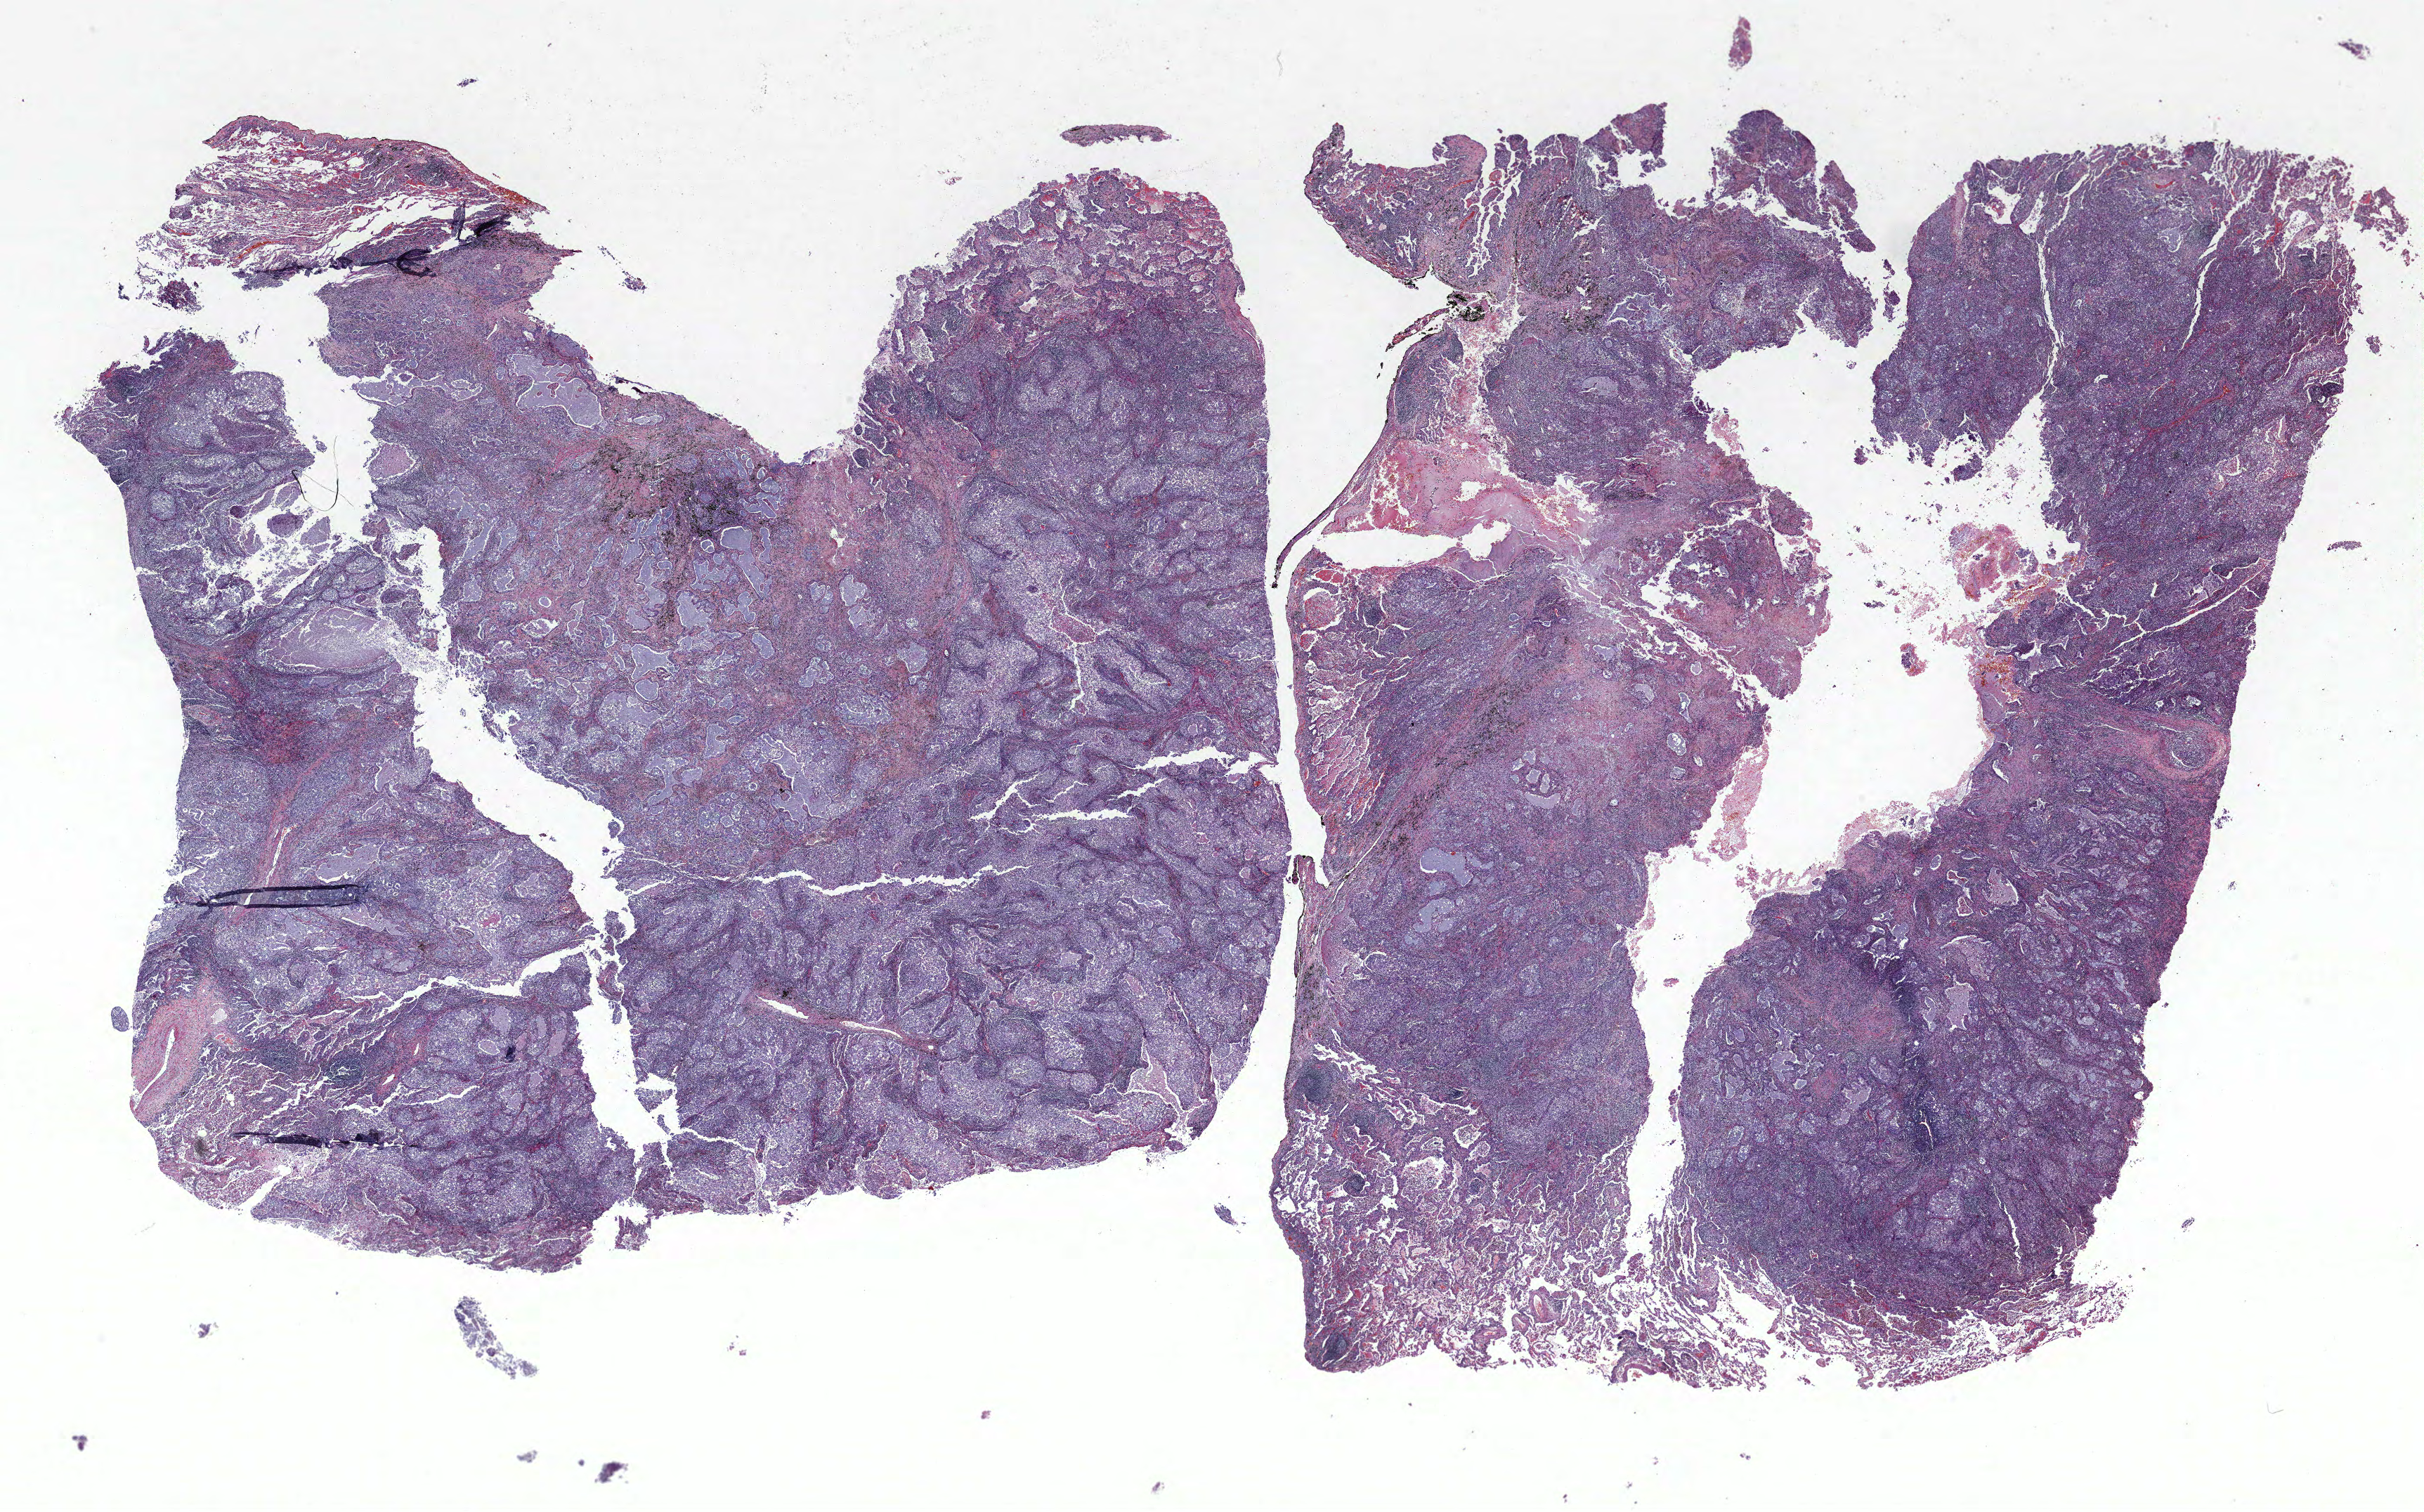
Whole-slide histology image, Hematoxylin and eosin (H&E) stained — low-resolution overview of the scanned area, about 27.6 x 17.2 mm (acquisition: 40x scan). Formalin-fixed paraffin-embedded (FFPE) section. Lung. Male patient, aged 71 at enrolment. Current smoker at enrolment. Grade: poorly differentiated (G3).
• stage (AJCC 6th edition): IIIB
• participant's lung-cancer diagnosis: Adenocarcinoma, NOS (ICD-O-3 8140/3)
• tumour size (pathology): 25 mm
• primary tumour location (clinical record): left upper lobe